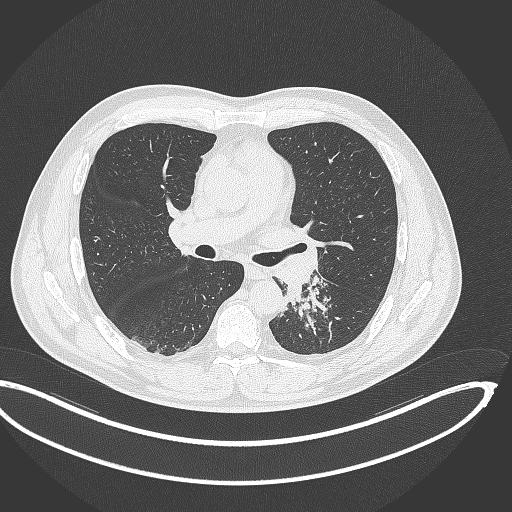
Chest CT, one axial slice. Lung window (W 1500 / L -600 HU). 1 mm slice thickness. 512 × 512 image matrix. Patient: male, 50 years. From the clinical record (not read from this slice): clinical TNM (as recorded): T2a N3 M0.
Outlined on this slice (rectangle marked by the reading radiologist):
- lung tumour (recorded histology: squamous cell carcinoma): bounding box (x1, y1, x2, y2) in pixels: (282, 282, 306, 308)